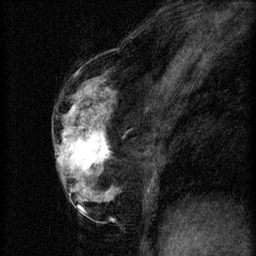
Breast MRI (dynamic contrast-enhanced), one sagittal slice; position 31 of 60 along the scan axis; 3 images stored at this slice position (order not interpretable as contrast timing); 1.5 T; TE 4.2 ms, TR 8.2 ms; 2 mm slice thickness; 256 × 256 image matrix, field of view 180 × 180 mm. Patient: female, 56 years.
Outlined on this slice (semi-automatically segmented with operator editing):
- analysis volume of interest (the breast-tissue region the enhancement analysis was run in; not a lesion): bounding box <60,124,112,179> (left, top, right, bottom; pixels)
- tumour enhancement mask (voxels above the 70 % enhancement threshold inside the analysis volume of interest): <63,132,109,169>